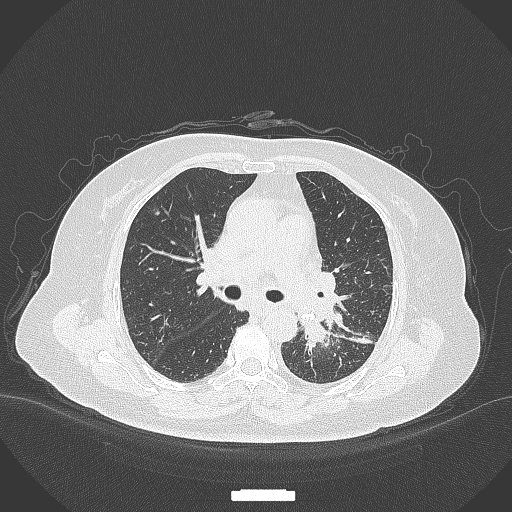
Chest CT, one axial slice; slice 213 of 322 in the series (ordered by position); 120 kVp; lung window (W 1500 / L -600 HU); 512 × 512 image matrix. Female patient, age 69 years. Case-level facts recorded for this patient, not image findings: clinical TNM (as recorded): T2b N3 M1.
Annotated regions visible in this slice (bounding box drawn by a radiologist):
- lung tumour (recorded histology: adenocarcinoma): bounding box [x1, y1, x2, y2] px = [294, 315, 331, 356]